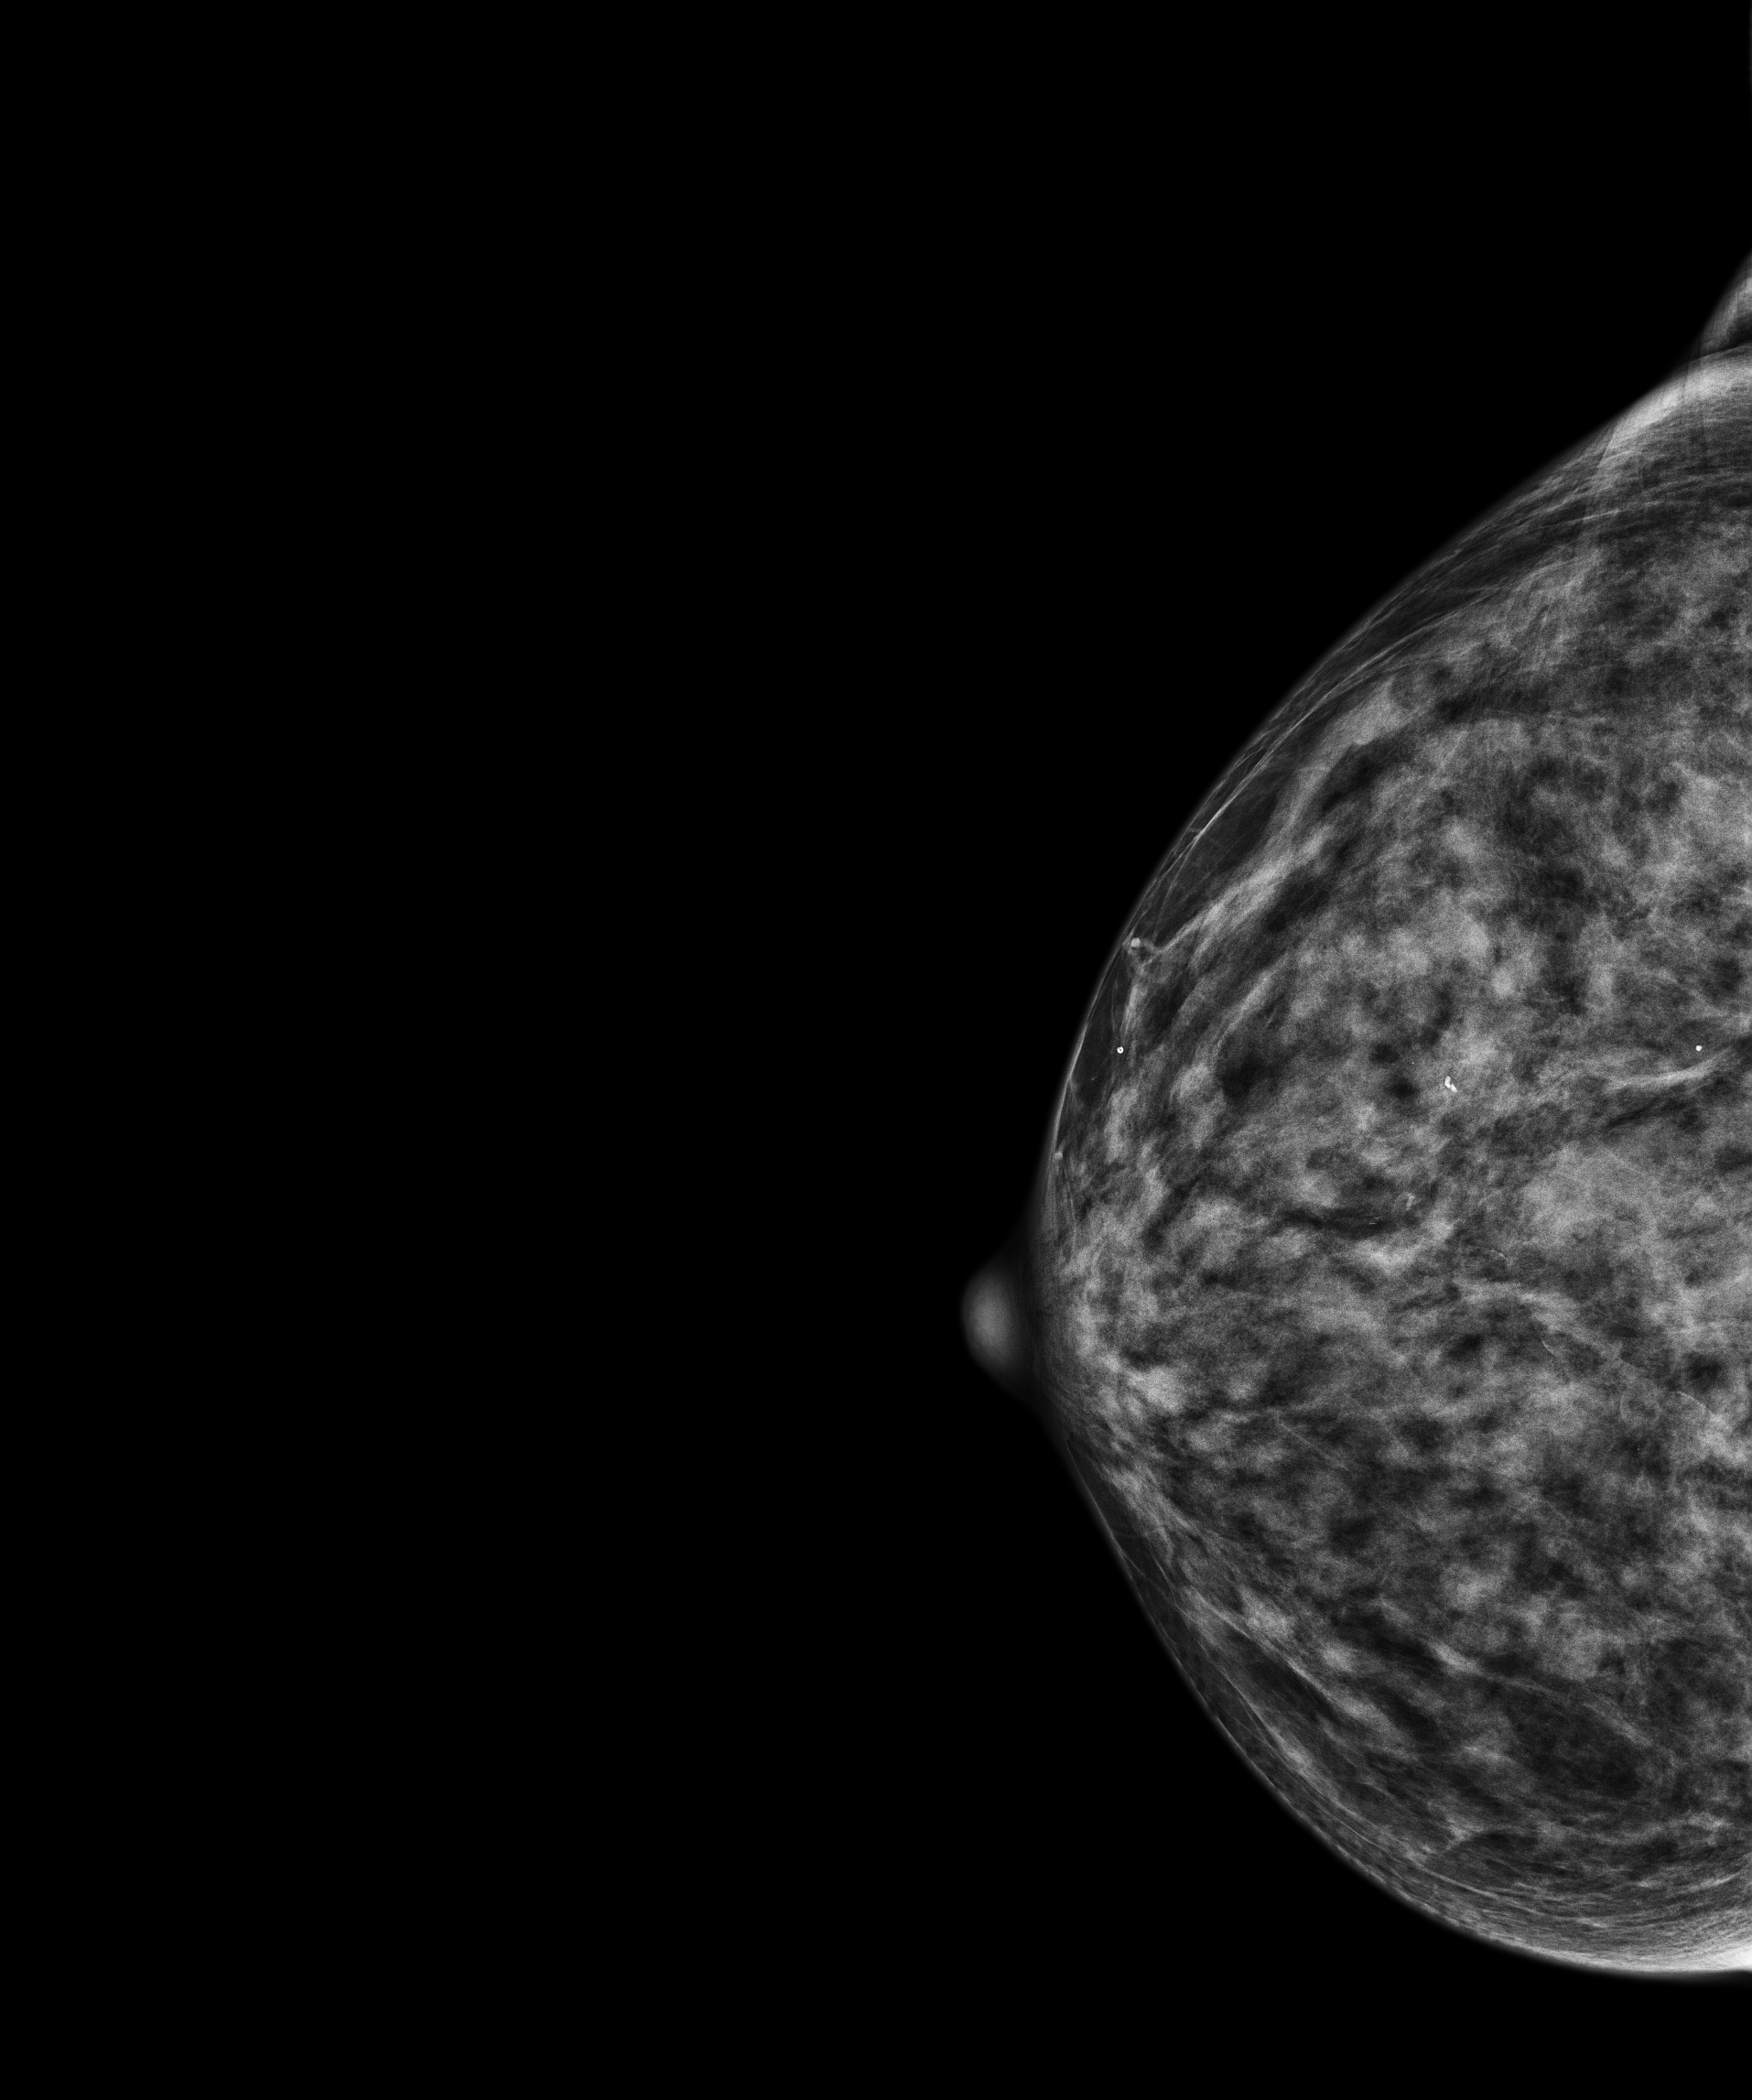
Annual screening mammography examination; system: Senographe Pristina. Female patient, age 74 years.
Image type: full-field digital mammogram. Breast: right. Projection: CC view.